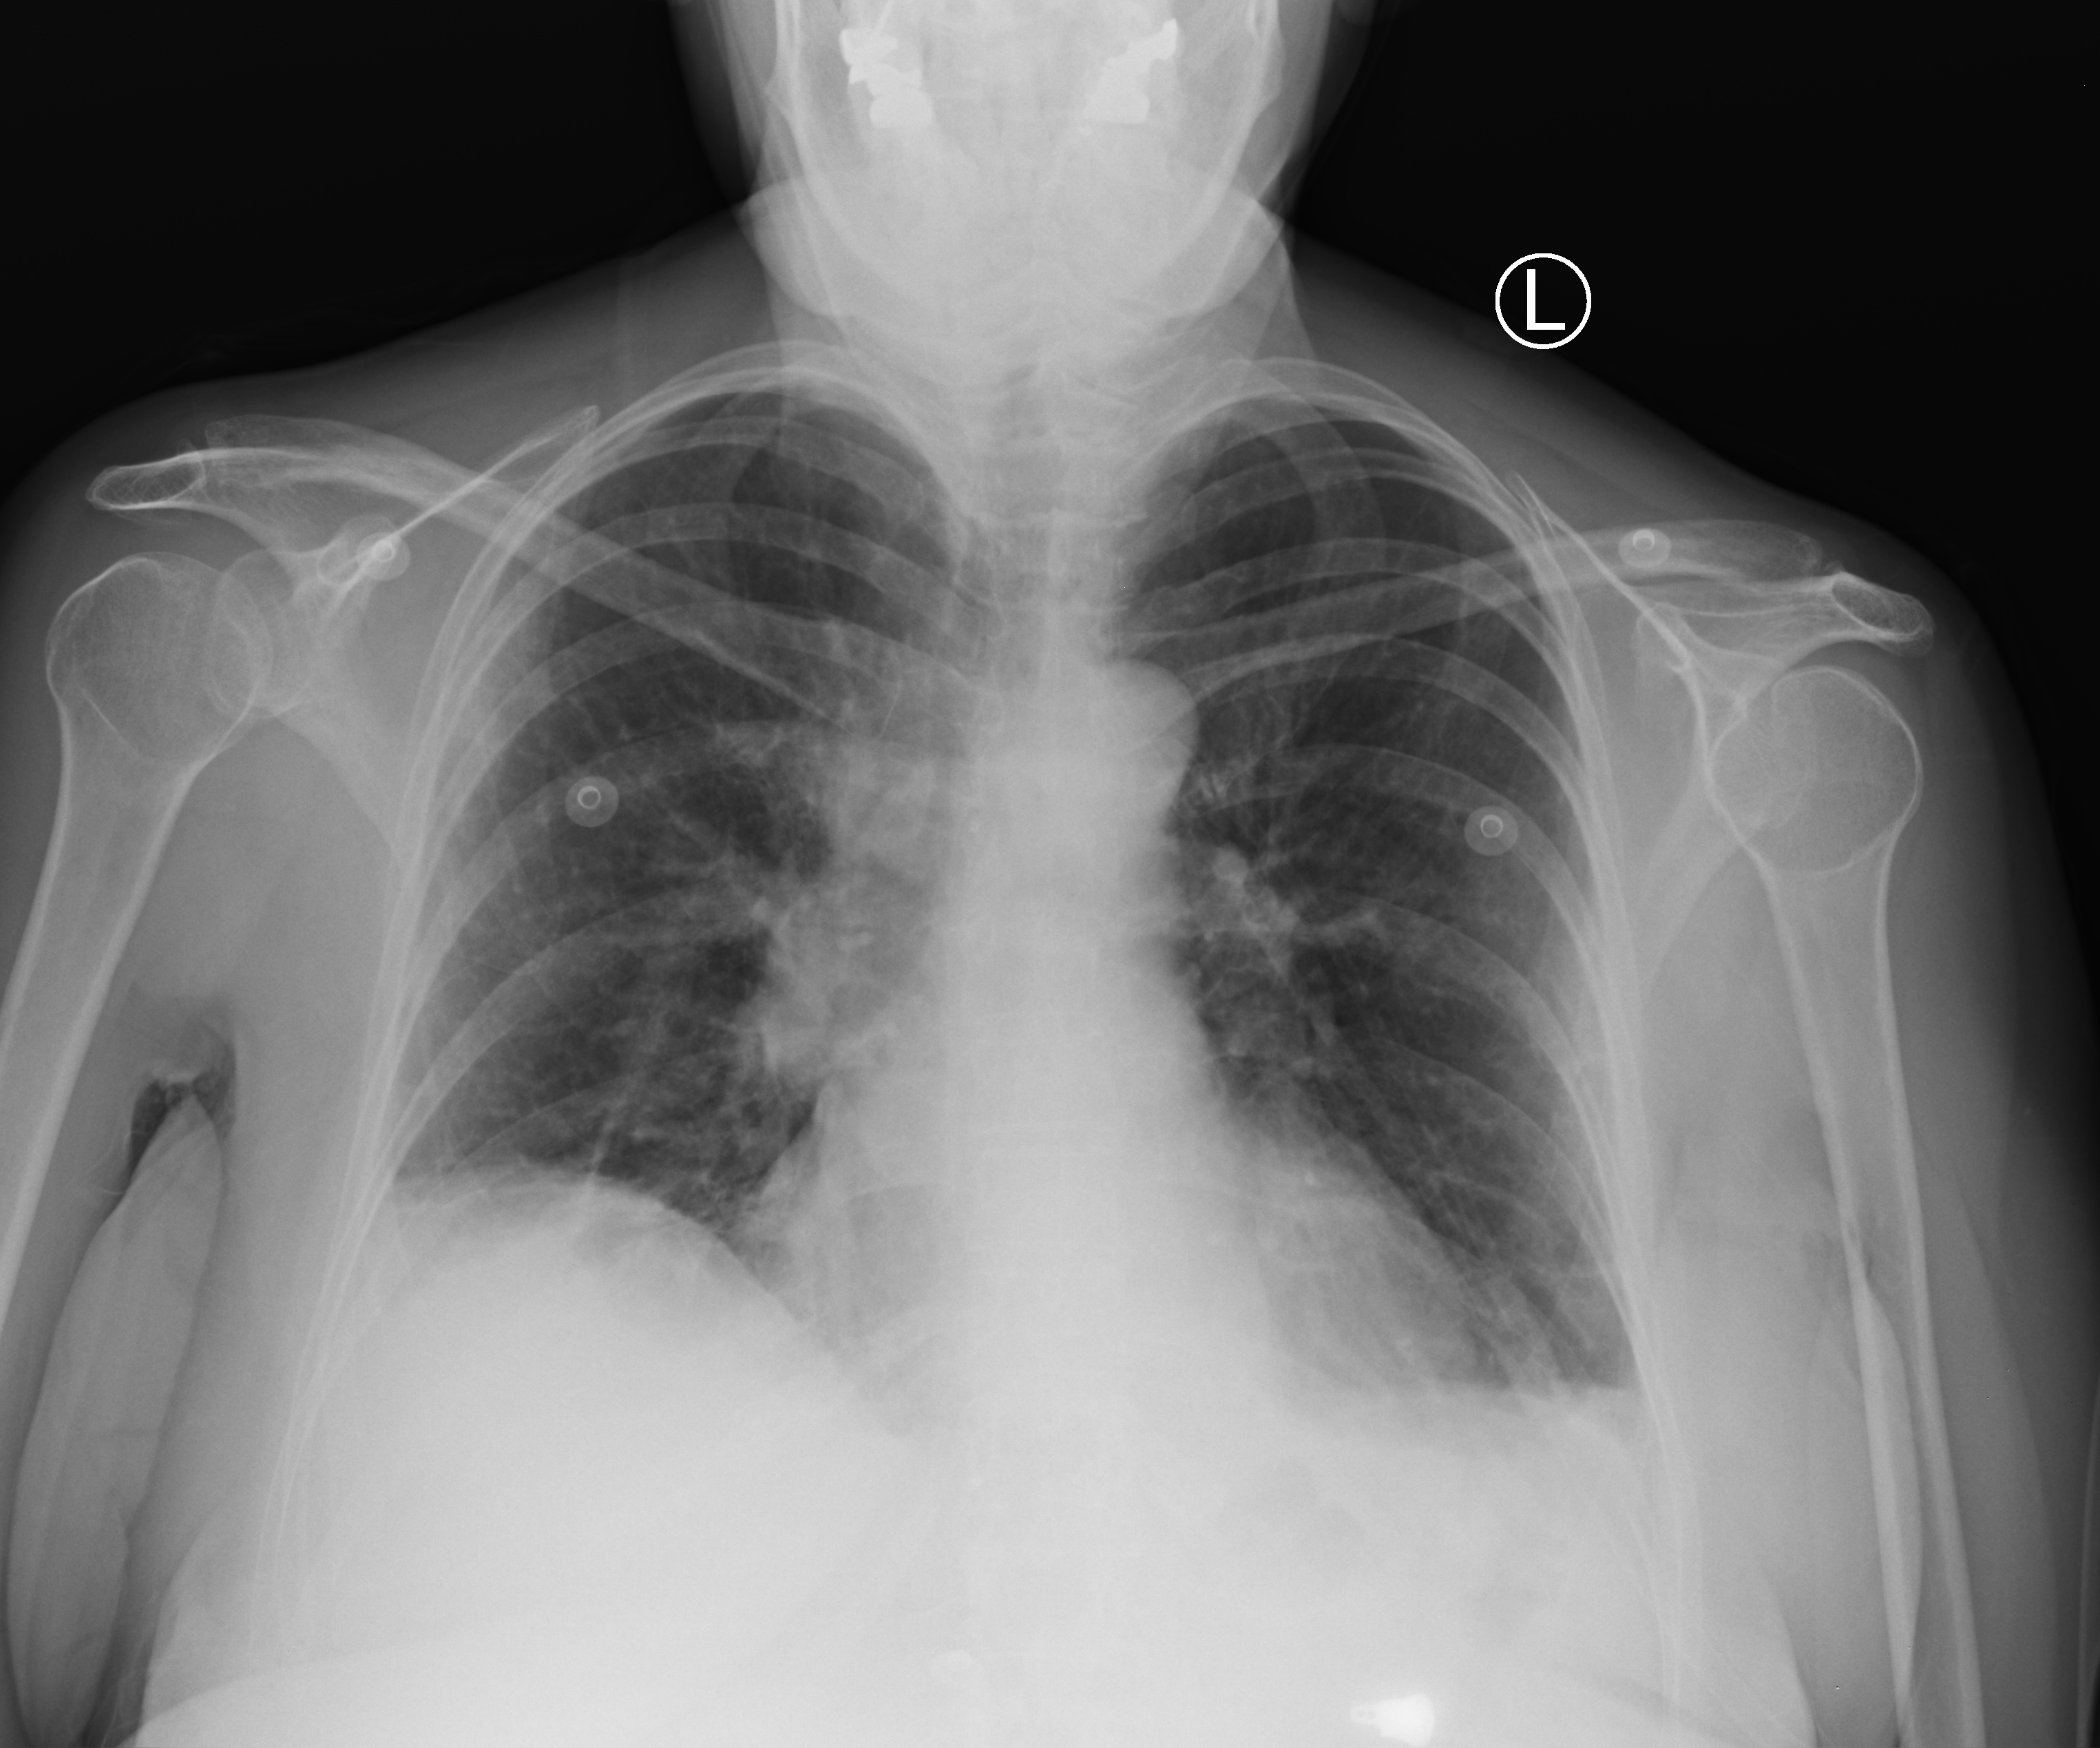
Portable chest radiograph; anteroposterior (AP) projection. Female patient hospitalised with COVID-19, age 60–74 years.
From the hospital-stay record, not from the radiograph (when in the stay this image was taken is not recorded): mechanically ventilated during this hospital stay: no; admitted to intensive care during this hospital stay: no; length of hospital stay: 6 days.